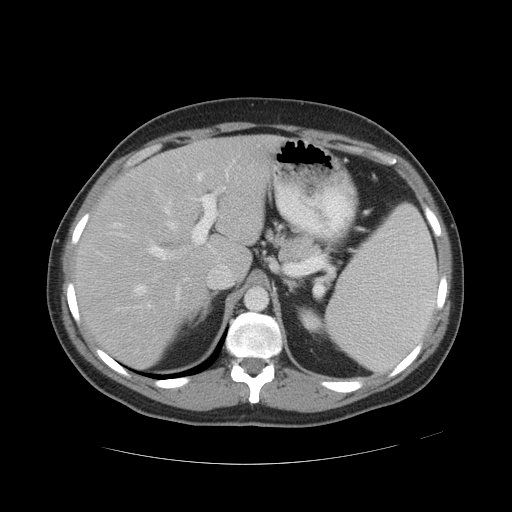
Contrast-enhanced abdominal CT, one axial slice. Slice 34 of 49 in the series (ordered by position). 120 kVp. Soft-tissue window (W 400 / L 40 HU). 5 mm slice thickness. 512 × 512 image matrix. Male patient, age 42 years. Case-level facts recorded for this patient, not image findings: diagnosis: colorectal cancer liver metastases, imaged before liver resection; multiple liver metastases: yes; largest metastasis: 2.8 cm; disease in both lobes: yes.
Structures marked on this image (outlined manually by an expert reader):
- hepatic veins: bounding box (x1, y1, x2, y2) in pixels: (135, 160, 240, 295)
- liver: (76, 136, 270, 368)
- planned liver remnant (the part of the liver to remain after resection): (76, 136, 270, 368)
- portal vein (with intrahepatic branches): (147, 176, 229, 308)
- liver metastasis: (127, 192, 134, 203)